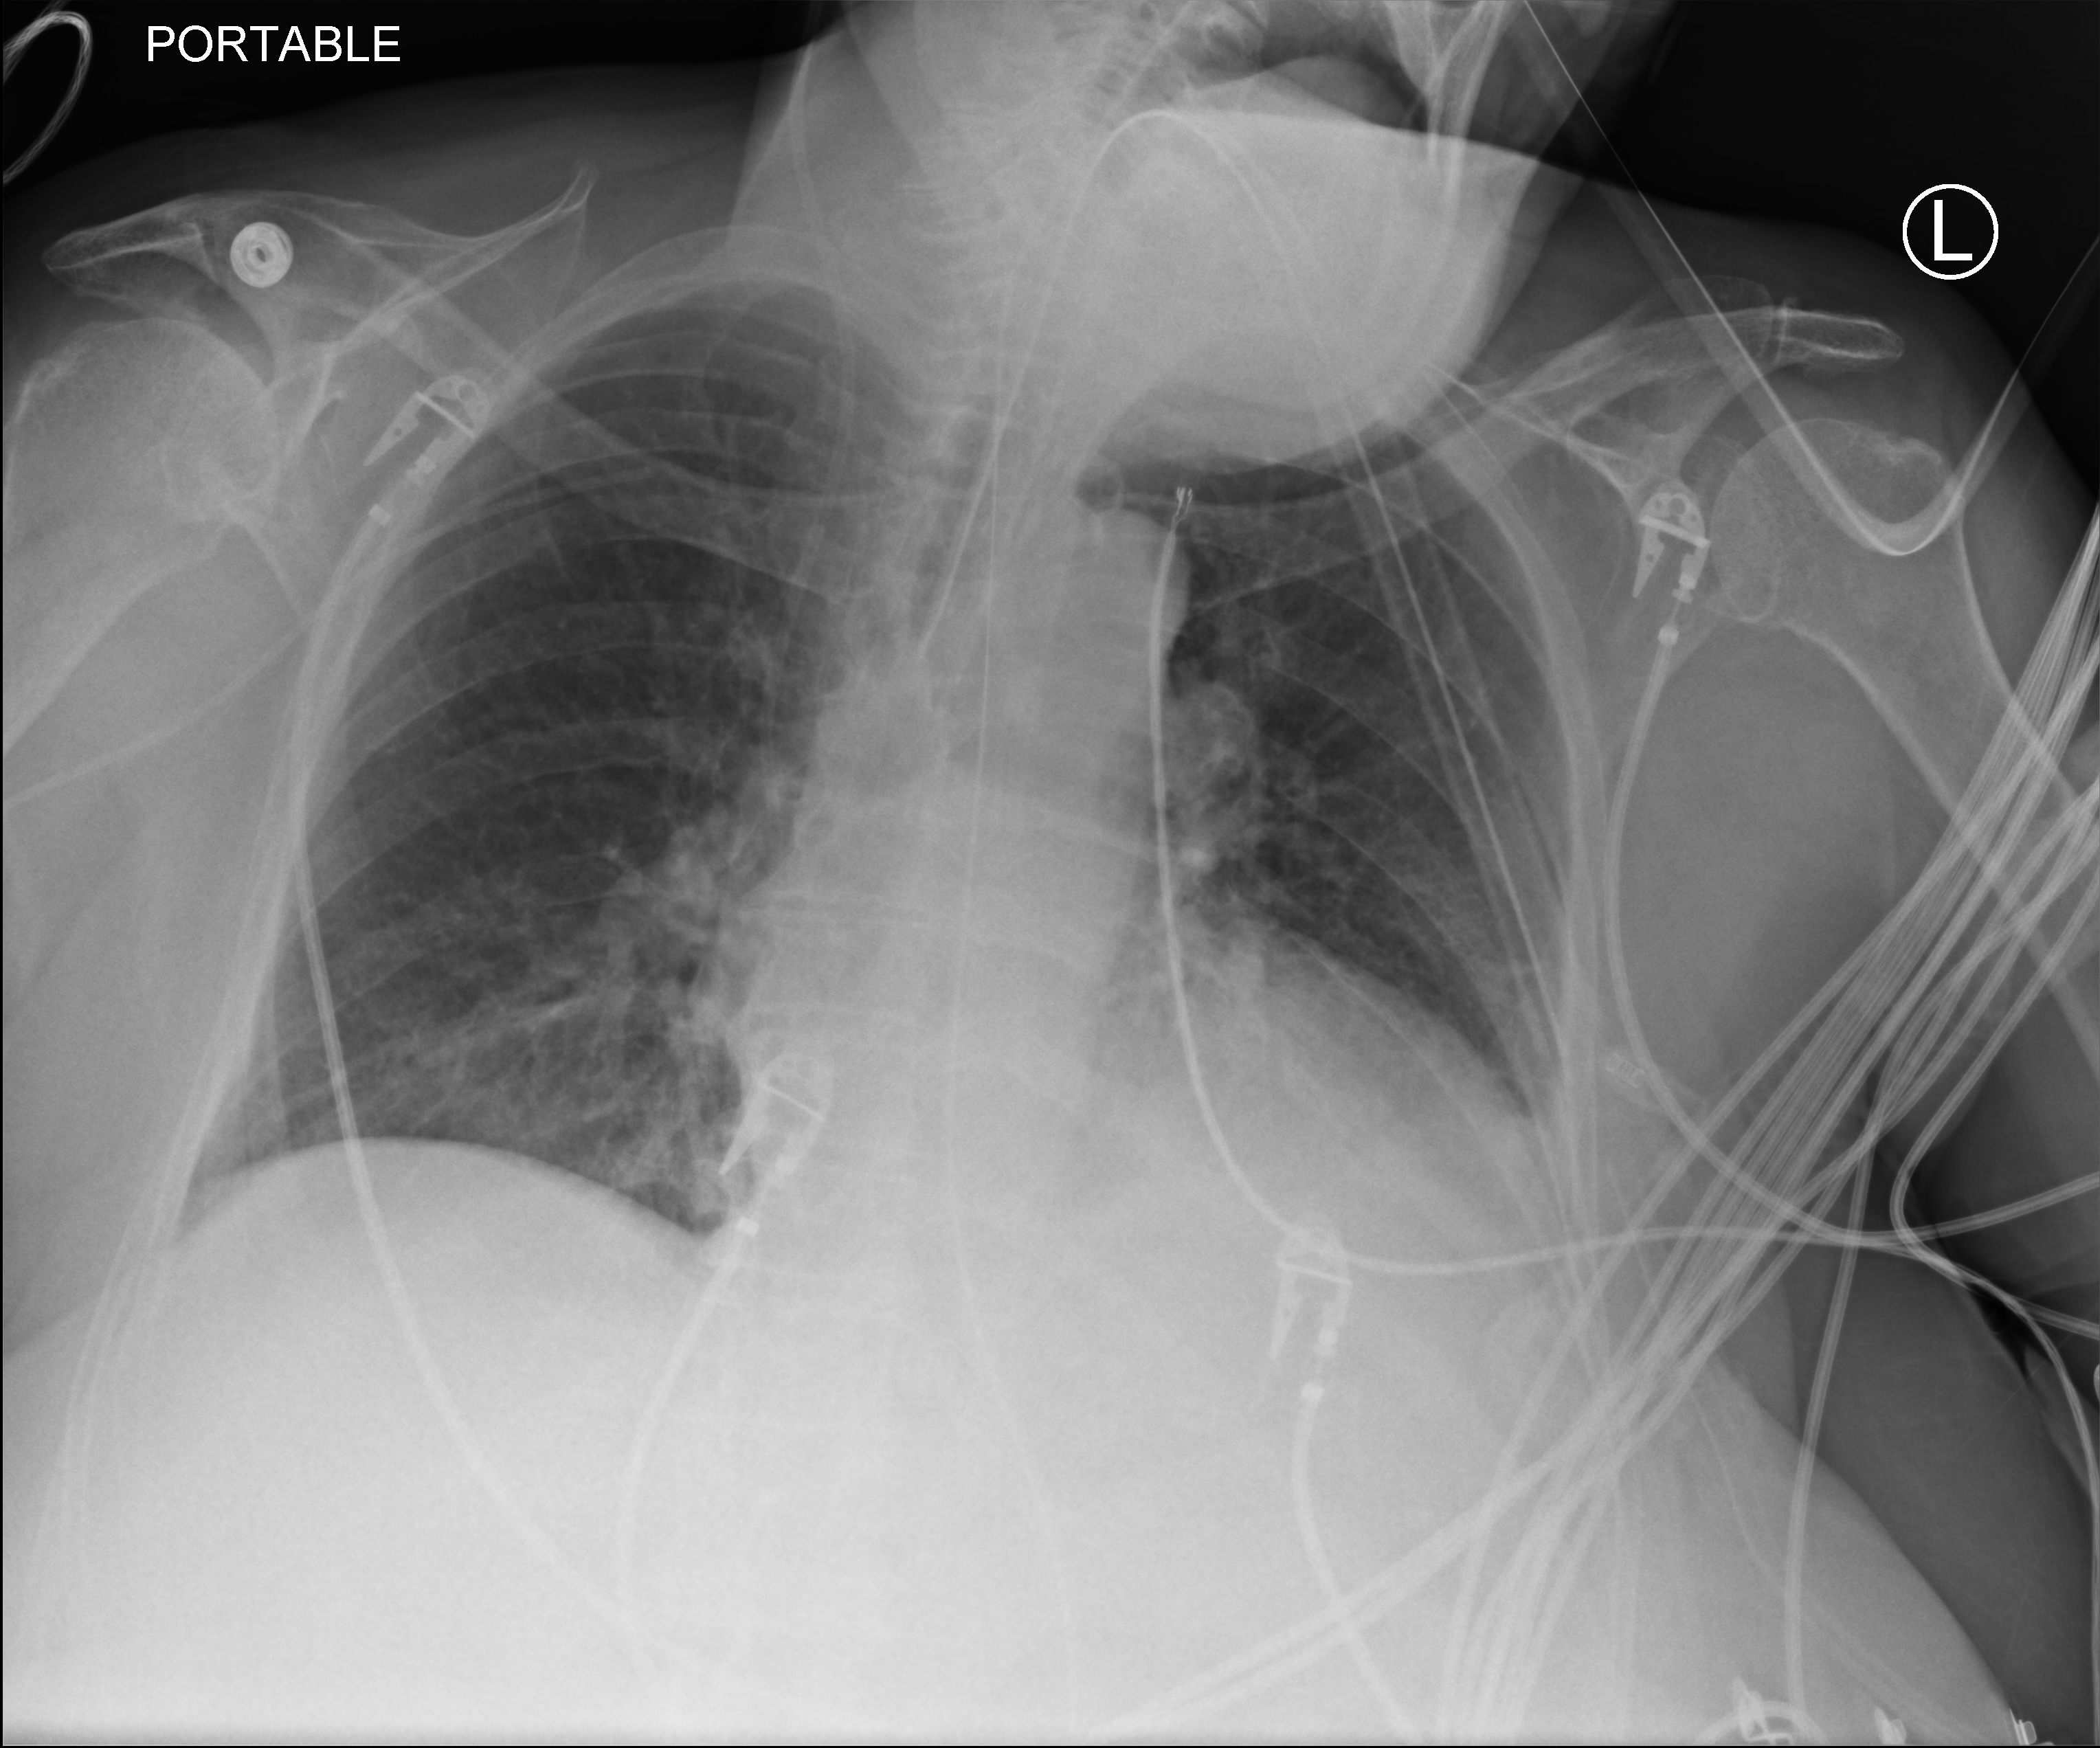
Chest X-ray (portable); anteroposterior (AP) projection. Female patient hospitalised with COVID-19, age 75–90 years.
From the hospital-stay record, not from the radiograph (when in the stay this image was taken is not recorded):
- mechanically ventilated during this hospital stay: yes
- admitted to intensive care during this hospital stay: yes
- COPD (admission record): no